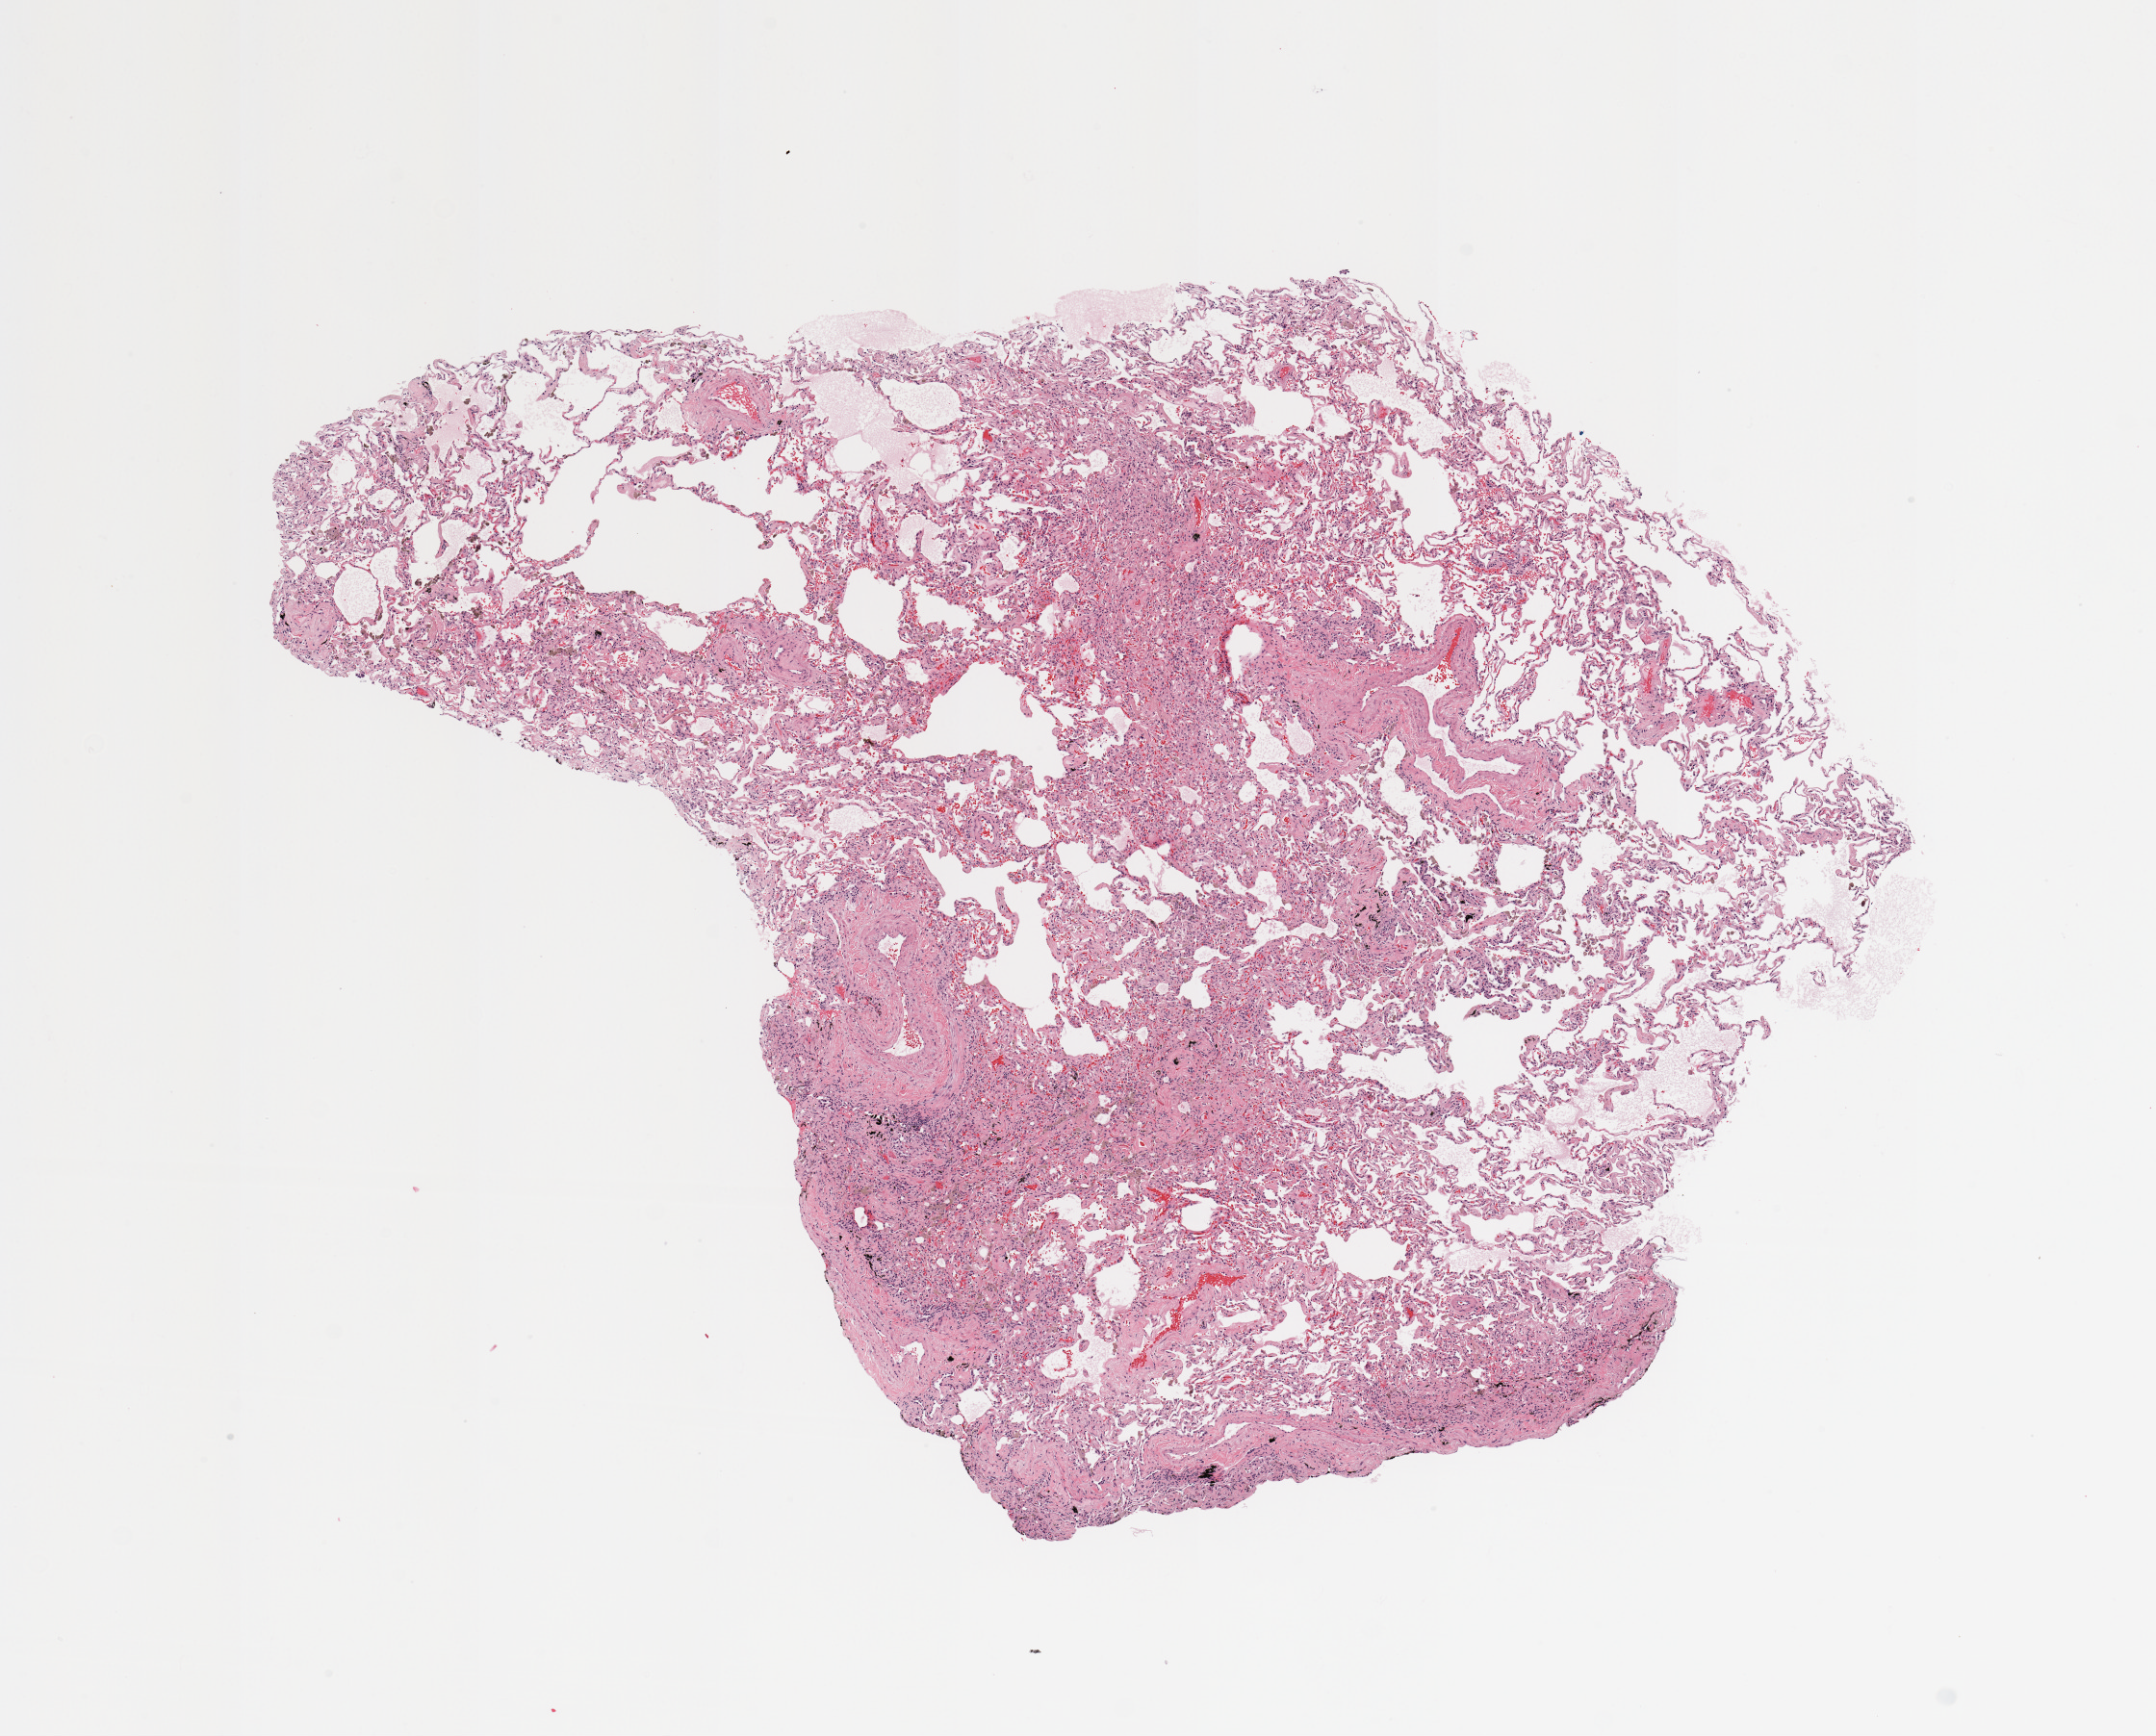
Whole-slide histology image, H&E — shown as a low-resolution overview of the whole scanned area (about 8.9 x 7.1 mm, acquisition: 20x scan). Normal (non-tumour) tissue sample, sampled site: lung. Patient: male, age 61 years.
This section: normal (non-tumour) tissue from the same patient. Patient diagnosis: Adenocarcinoma, NOS.